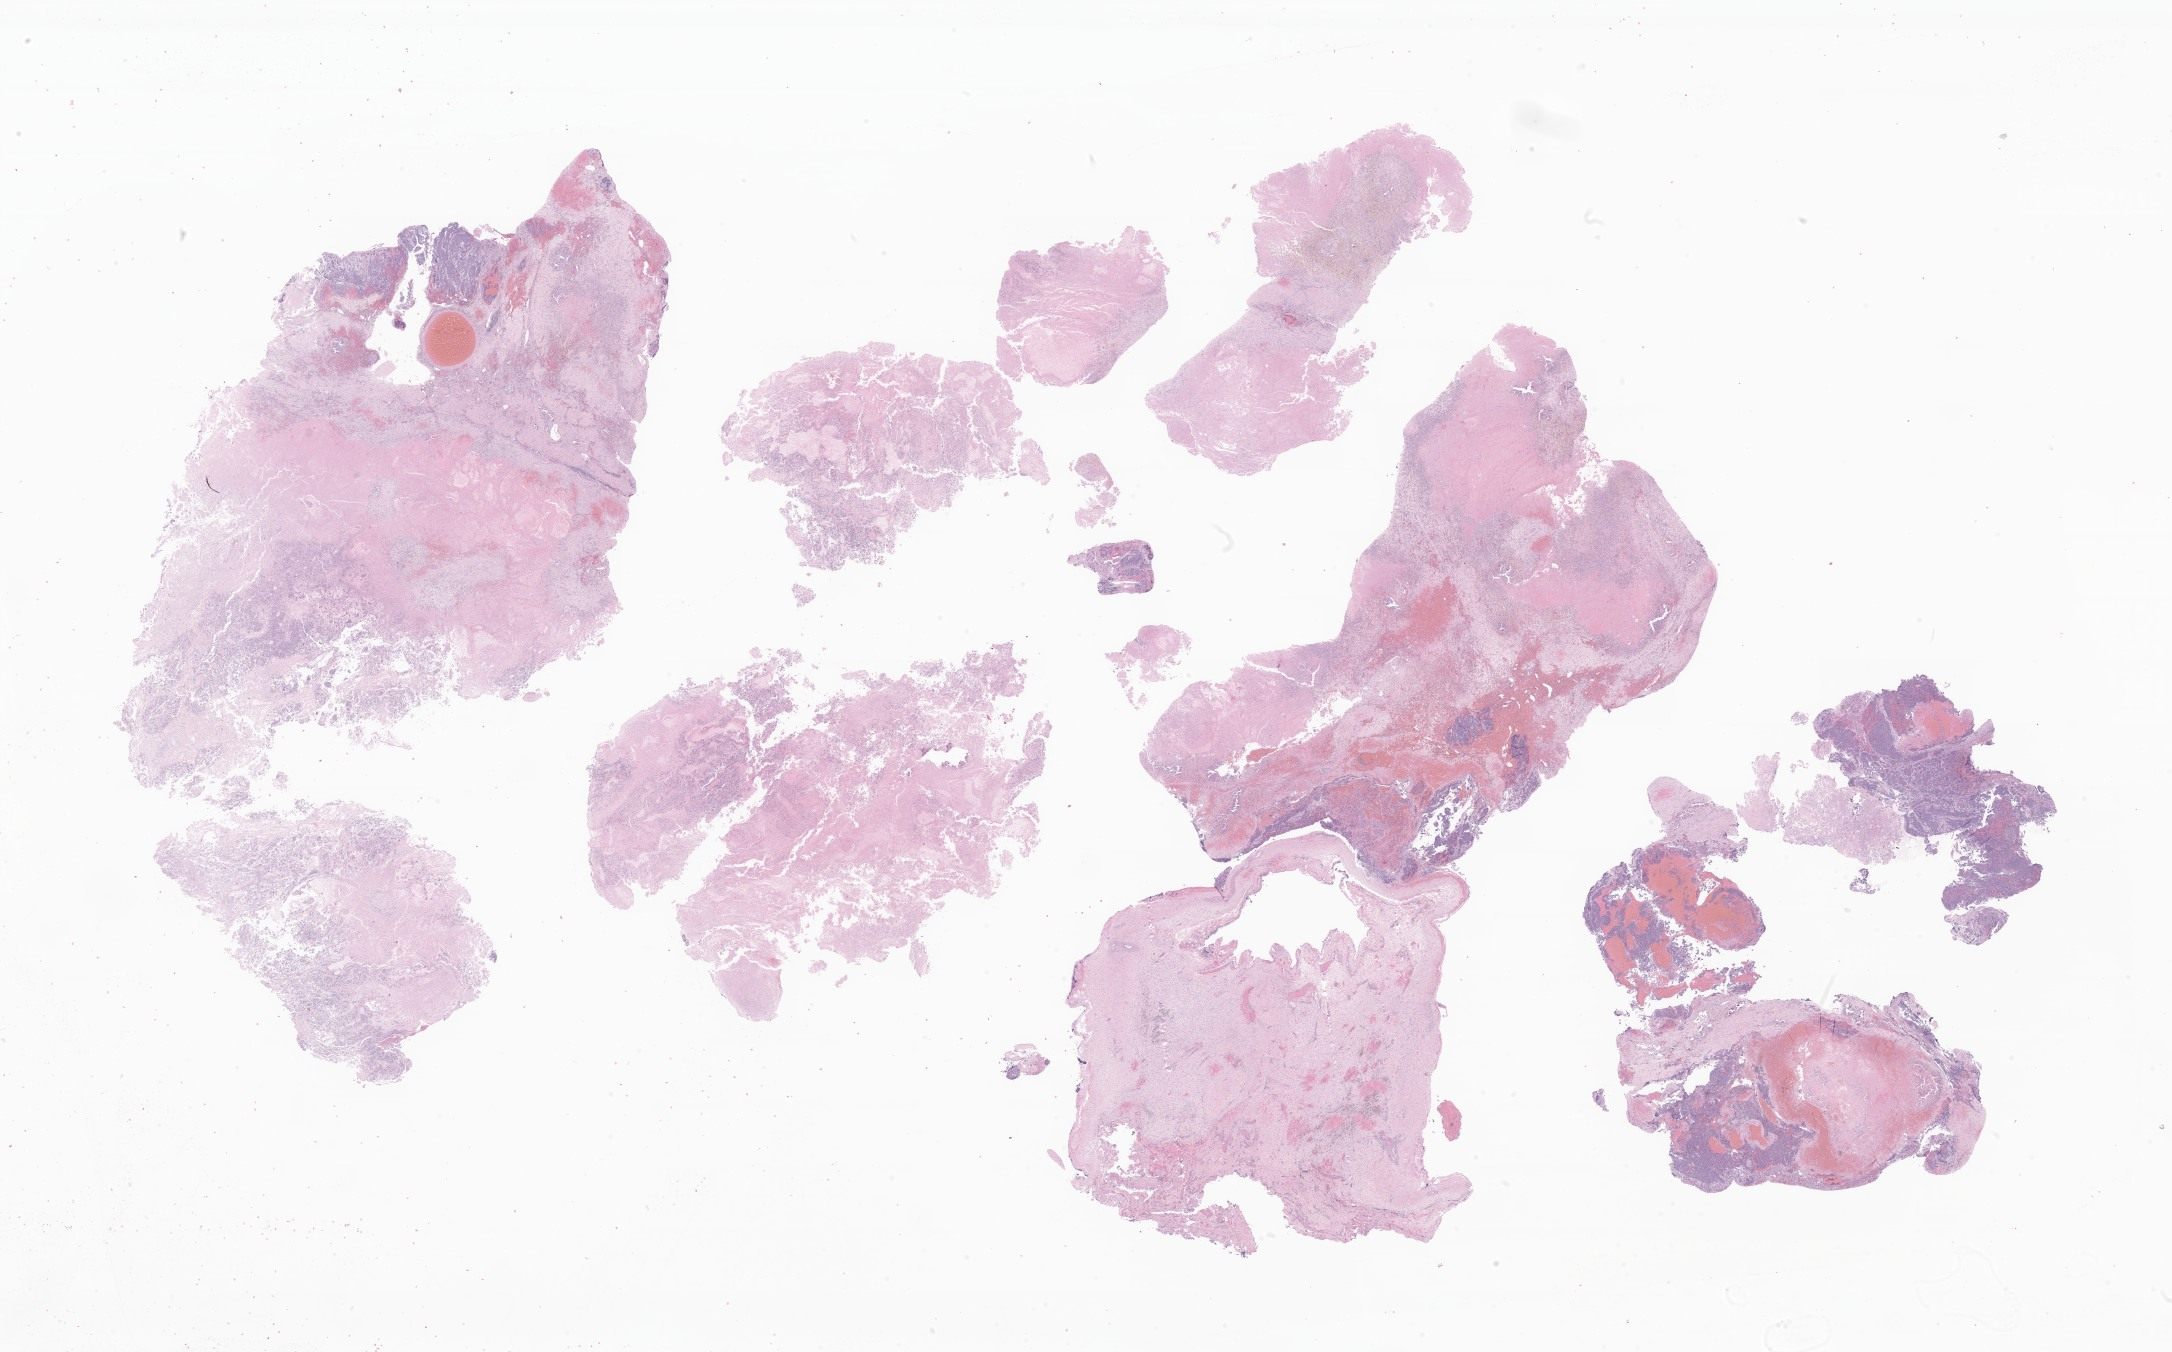
Digitized haematoxylin and eosin-stained section of tumor tissue from the adrenal gland, whole scanned area (about 36.6 x 22.8 mm) shown as a low-resolution overview; FFPE section. Patient: female, age 150 days.
Diagnosis (ICD-O-3 morphology term): Neuroblastoma, NOS.